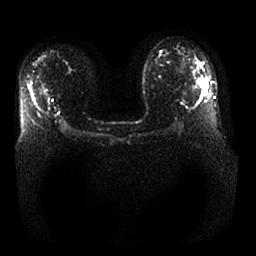
Breast MRI, one axial slice. Position 18 of 25 along the scan axis. Diffusion-weighted series; image 2 of 4 stored at this slice position (different b-values; order by instance number). 1.5 T. 256 × 256 image matrix. Female patient.
Annotated regions visible in this slice (outlined manually by an expert reader):
- tumour on diffusion-weighted imaging: bounding box [x1, y1, x2, y2] px = [199, 80, 207, 87]